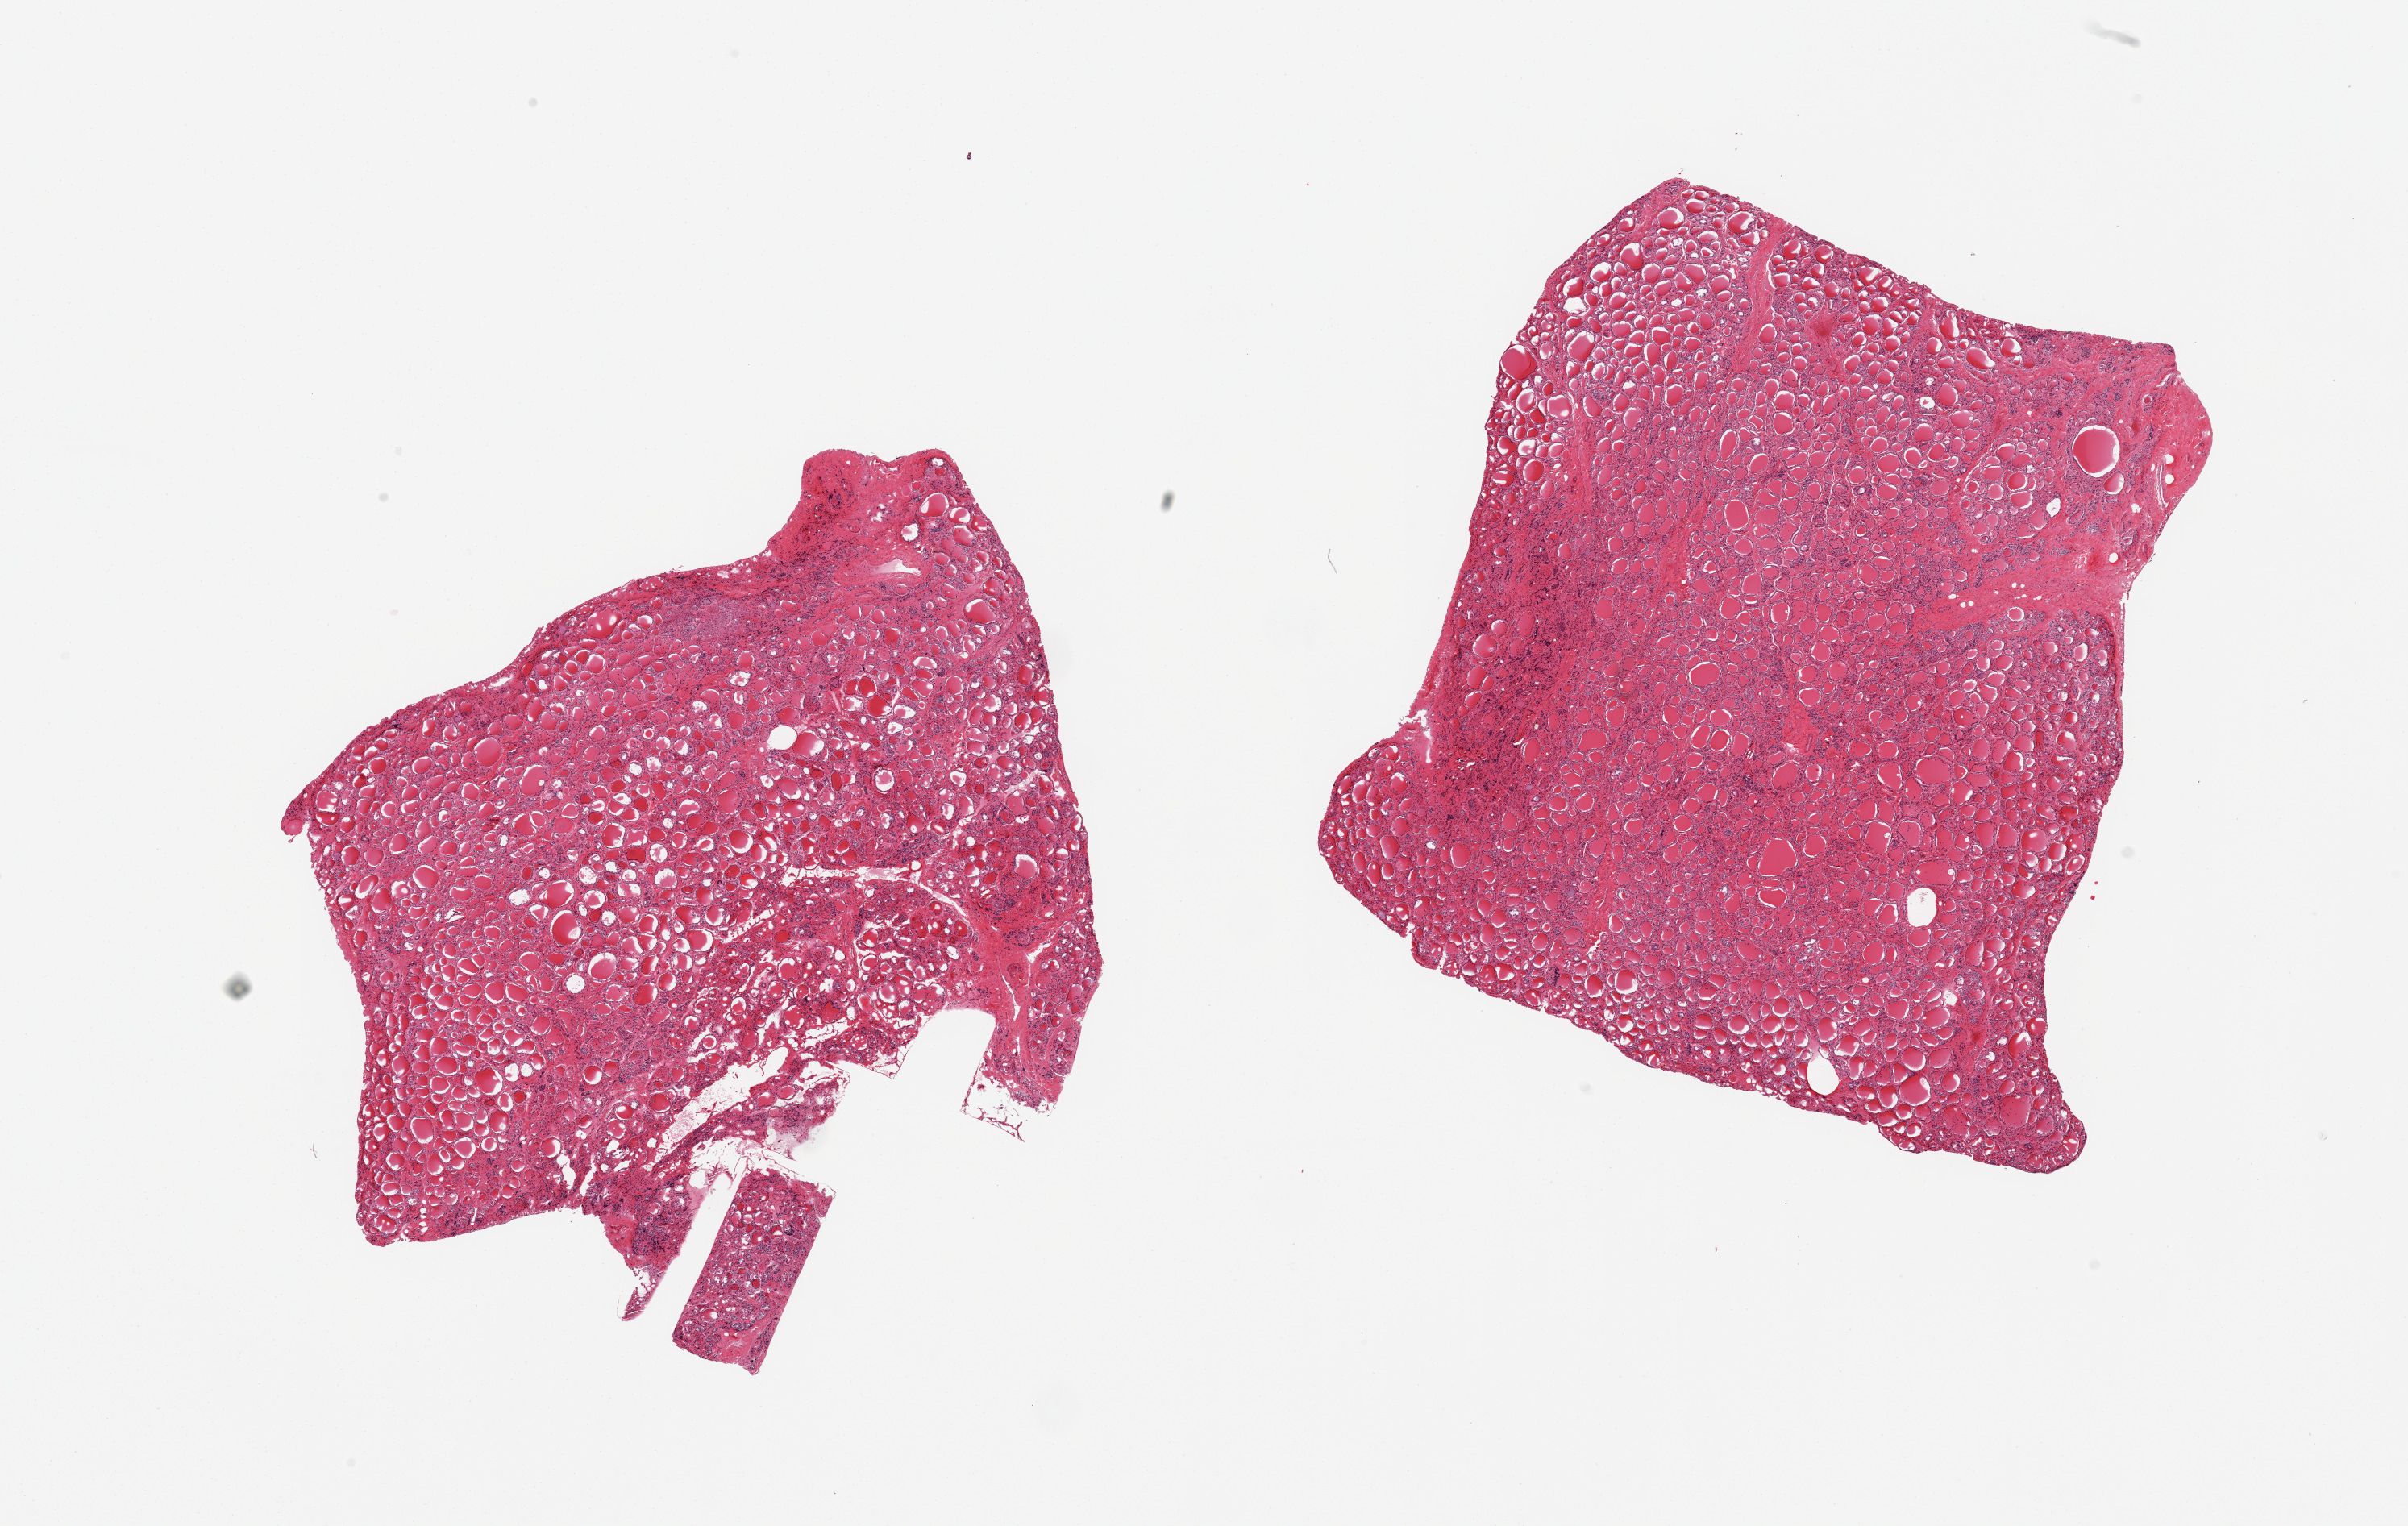
Whole-slide image, haematoxylin and eosin stain — whole scanned area (about 23.6 x 15.0 mm) shown as a low-resolution overview, PAXgene-fixed paraffin-embedded (PFPE) section, sampled site (target tissue): thyroid, tissue donor sample. Donor sex: male.
Review note (as recorded): 2 pieces.